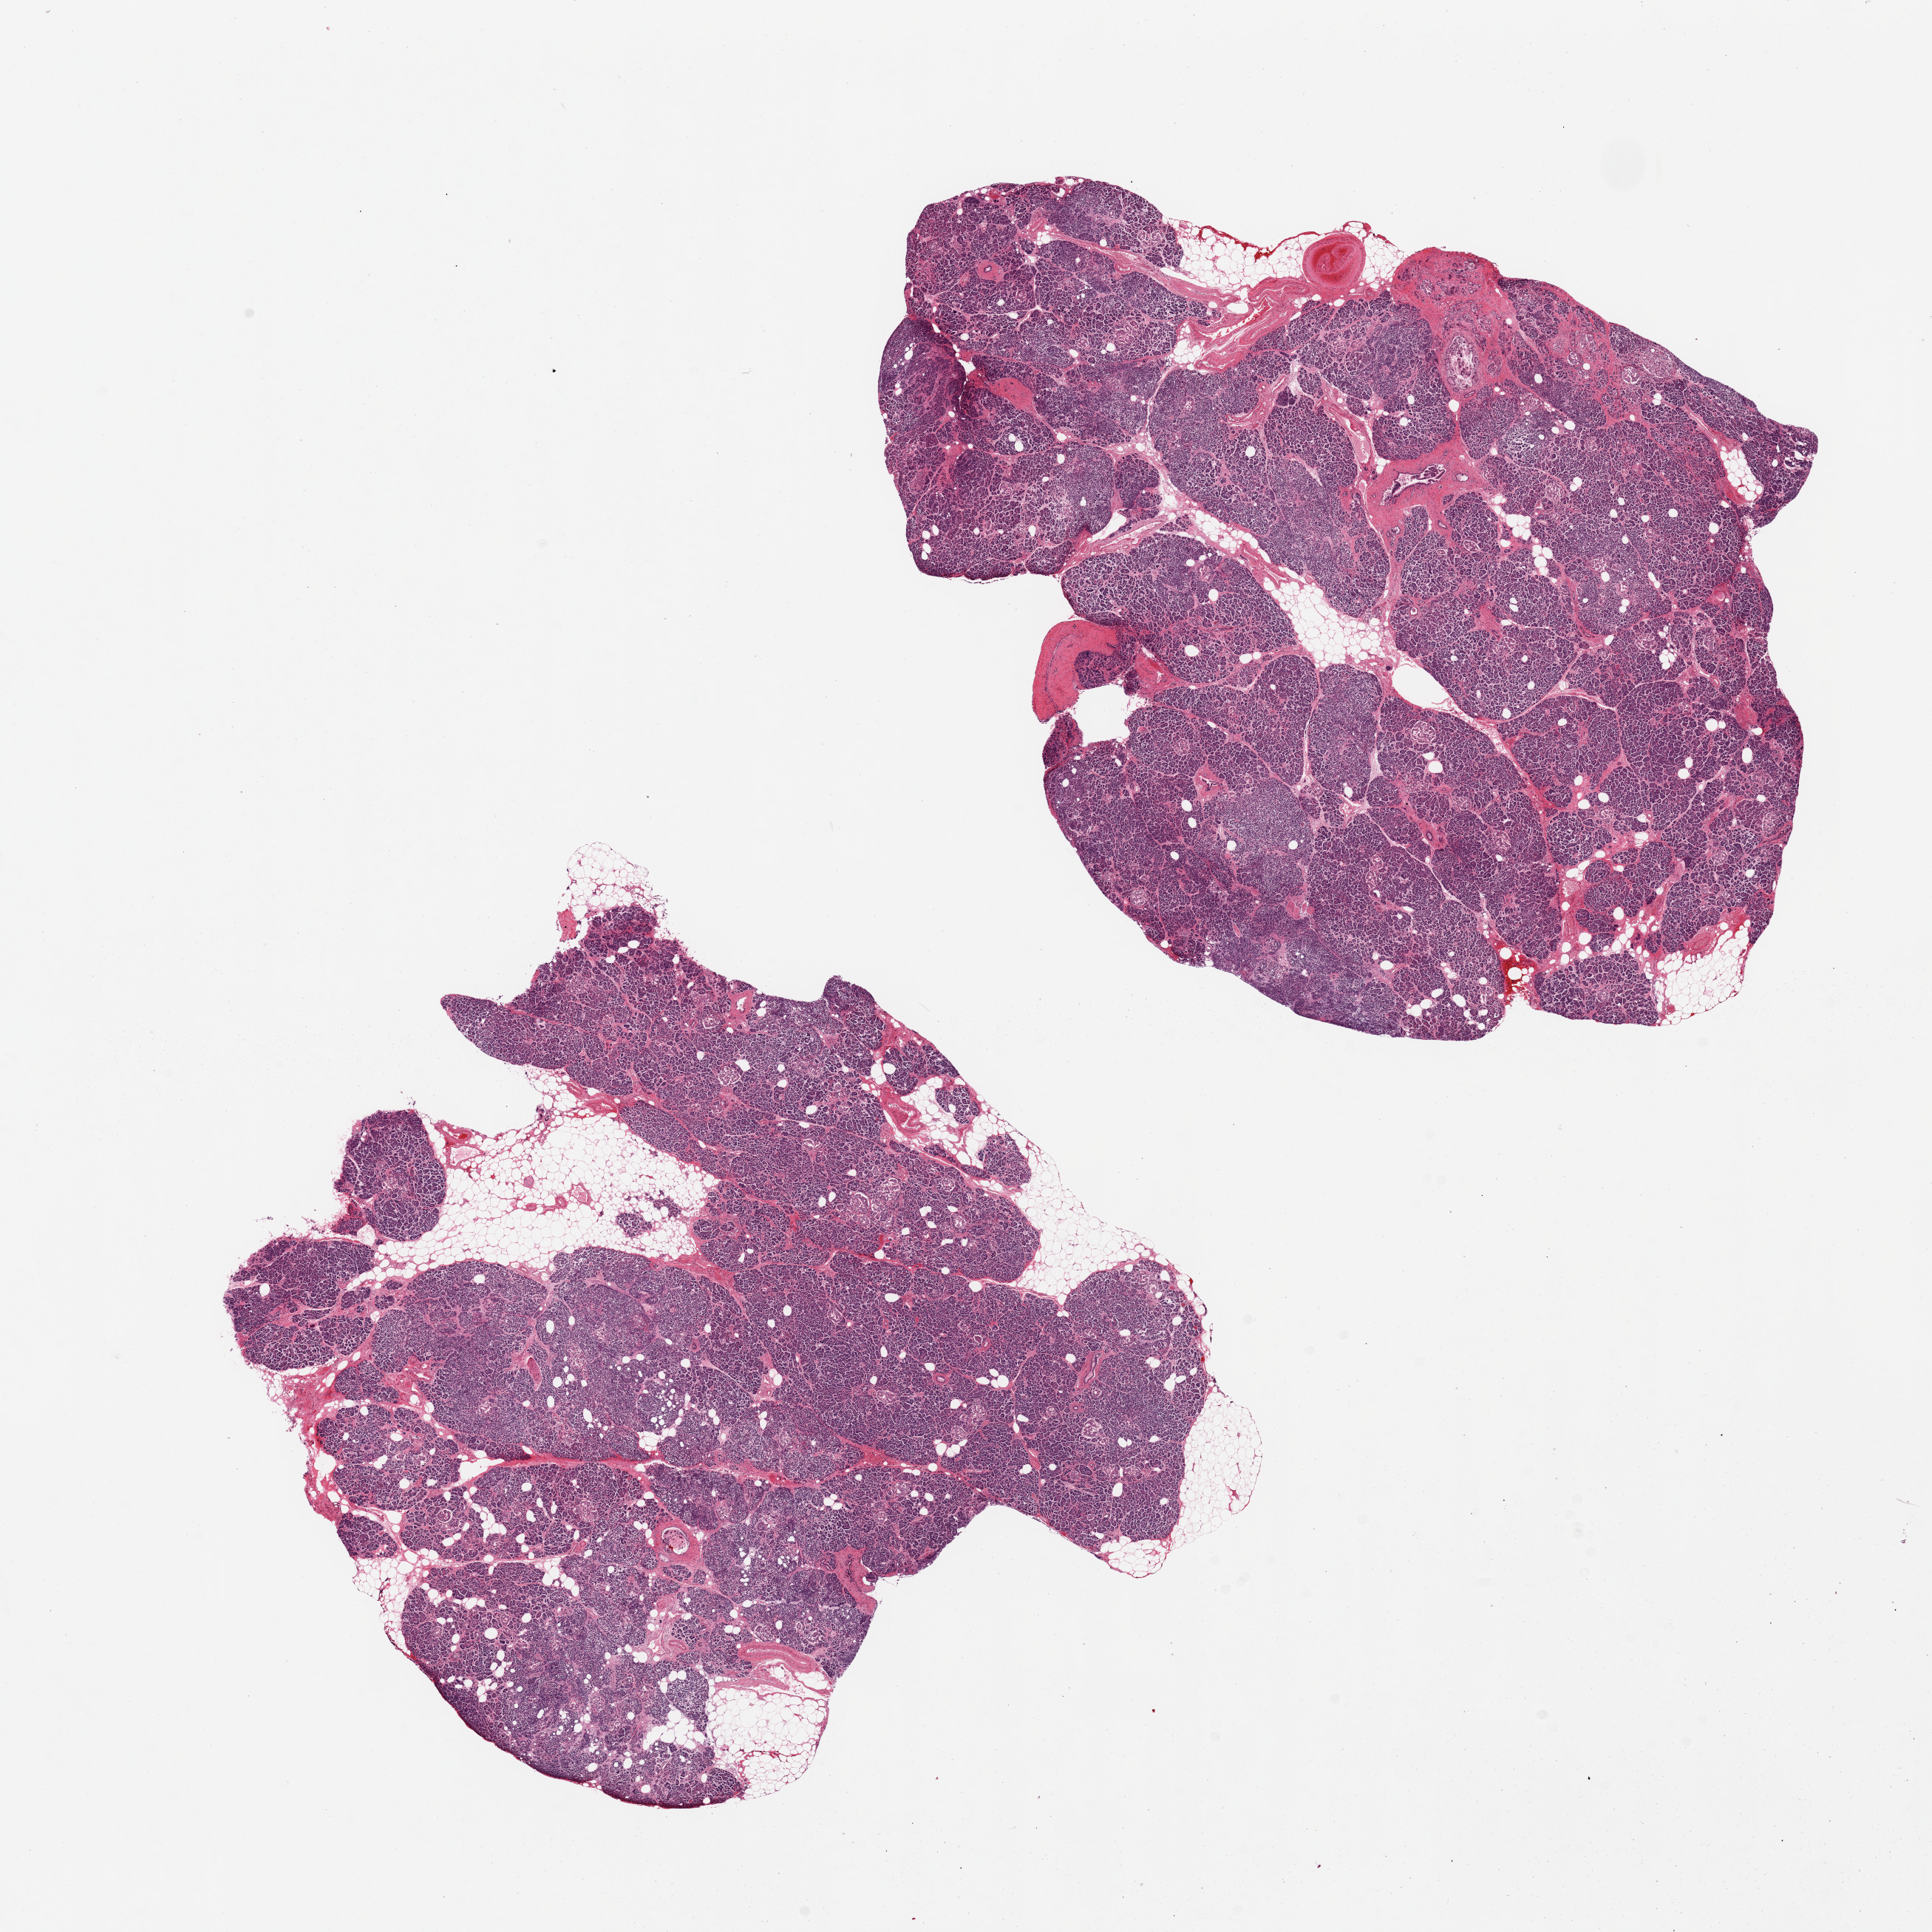
Digitized haematoxylin and eosin-stained section, brightfield, whole scanned area (about 20.7 x 20.7 mm) shown as a low-resolution overview. PAXgene-fixed paraffin-embedded (PFPE) section. Target tissue: pancreas. Tissue donor sample.
Reviewer comment on this tissue sample: 2 pieces, moderate autolysis.